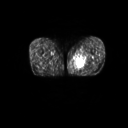
FDG PET of an extremity soft-tissue mass (from a PET/CT study), one axial slice; position 15 of 267 along the scan axis; 3.27 mm slice thickness; 128 × 128 image matrix. Patient: male, 59 years. From the clinical record (not read from this slice): histological type: pleiomorphic liposarcoma; grade: high; site of the primary tumour: left thigh.
Outlined on this slice (expert contour drawn on MRI and transferred to this co-registered scan by the dataset authors):
- gross tumour volume including surrounding oedema: box from (x=74, y=53) to (x=89, y=70) px
- gross tumour volume (mass): (x=76, y=61)–(x=86, y=69)